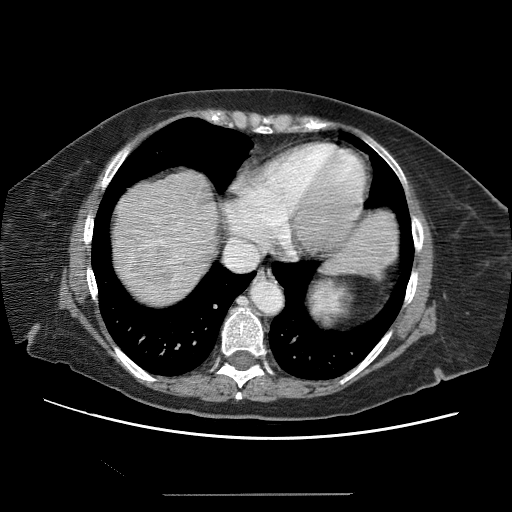
Contrast-enhanced abdominal CT (liver protocol), one axial slice; position 57 of 65 along the scan axis; soft-tissue window (W 400 / L 40 HU); 2.5 mm slice thickness; 512 × 512 image matrix, field of view 380 × 380 mm. Case-level facts recorded for this patient, not image findings: diagnosis: hepatocellular carcinoma (patient treated with transarterial chemoembolisation; whether this scan precedes or follows treatment is not stated here); TNM stage (as recorded): Stage-IIIB; Child-Pugh class: A; tumour differentiation: moderately differentiated; tumour nodularity: uninodular.
Outlined on this slice (semi-automatically segmented with operator editing):
- abdominal aorta: box from (x=255, y=283) to (x=284, y=316) px
- liver parenchyma outside the tumour (the mass and vessels are separate outlines, so this box may not span the whole liver): (x=118, y=172)–(x=216, y=286)
- mass: (x=122, y=240)–(x=196, y=299)
- liver vessels: (x=142, y=196)–(x=211, y=256)